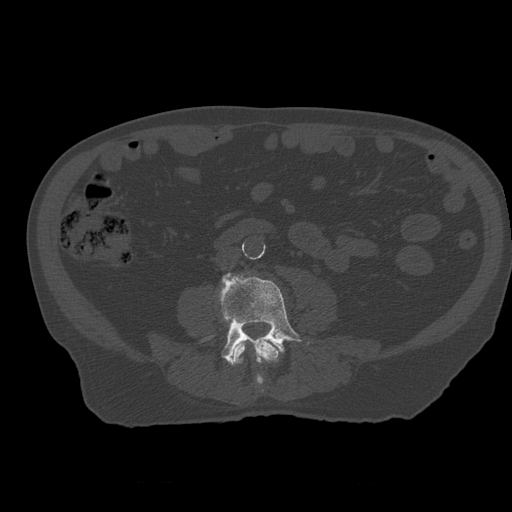
CT including the spine, one axial slice. Slice 171 of 399 in the series (ordered by position). Bone window (W 1800 / L 400 HU). 1.25 mm slice thickness. 512 × 512 image matrix, field of view 407 × 407 mm. Patient age 73 years. Case-level facts recorded for this patient, not image findings: primary cancer: prostate; vertebrae with lytic lesions (as recorded): L2.
Outlined on this slice (semi-automatically segmented with operator editing):
- L3 vertebra: bounding box (x1, y1, x2, y2) in pixels: (234, 339, 280, 393)
- L4 vertebra: (220, 272, 311, 366)